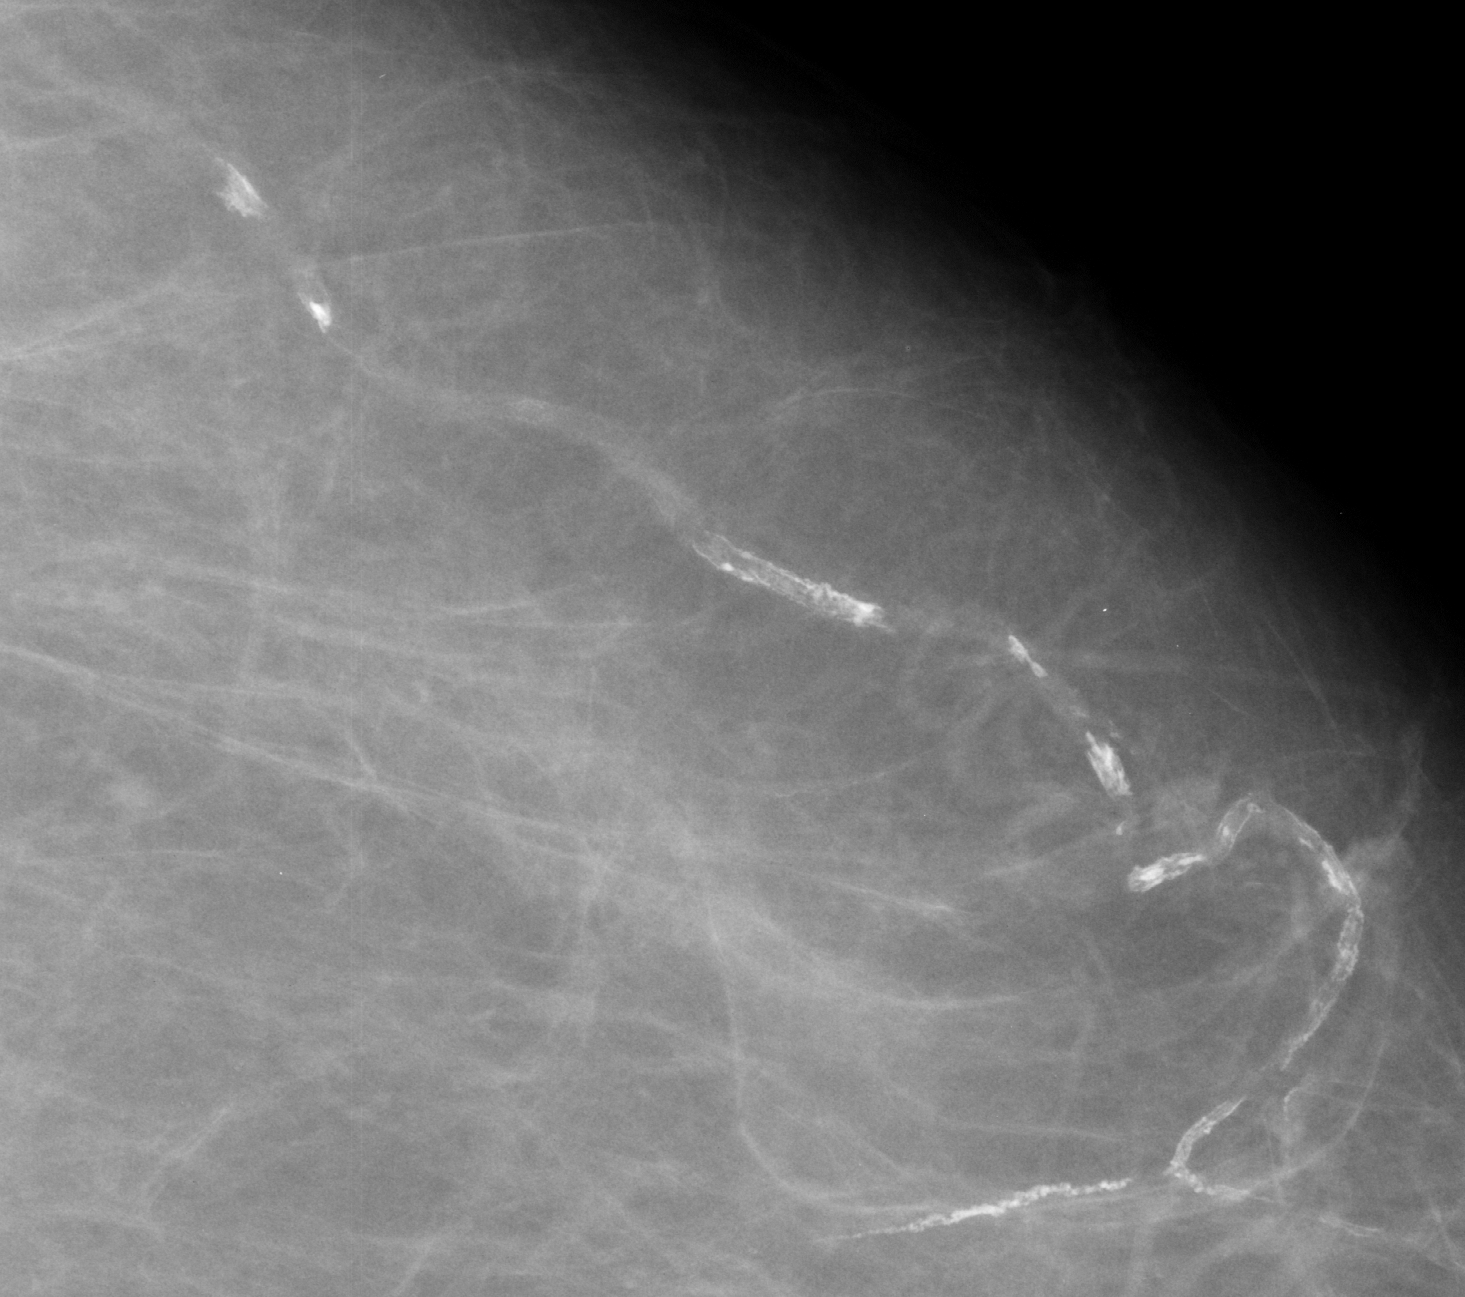
Cropped region of a digitized screen-film mammogram centred on a radiologist-marked abnormality; left breast; CC view; BI-RADS breast density category 1 (scale 1–4).
Calcifications, morphology vascular; BI-RADS assessment category 2; subtlety rating 5 on a 1 (subtle) to 5 (obvious) scale; benign; no additional work-up was recommended (benign without callback).